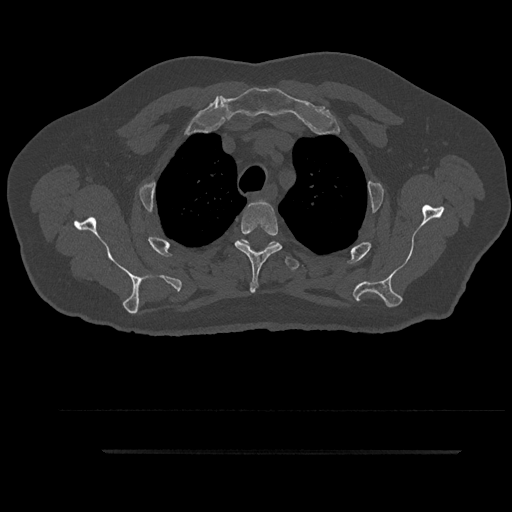
CT including the spine, one axial slice. Slice 710 of 797 in the series (ordered by position). Reconstruction kernel Br40s/3. Bone window (W 1800 / L 400 HU). 512 × 512 image matrix, field of view 432 × 432 mm. Male patient, age 63 years. From the clinical record (not read from this slice): primary cancer: renal; vertebrae with lytic lesions (as recorded): T8.
Structures marked on this image (semi-automatic segmentation, software-assisted and operator-edited):
- T3 vertebra: bounding box [x1, y1, x2, y2] px = [235, 199, 282, 293]
- T4 vertebra: [243, 240, 299, 270]